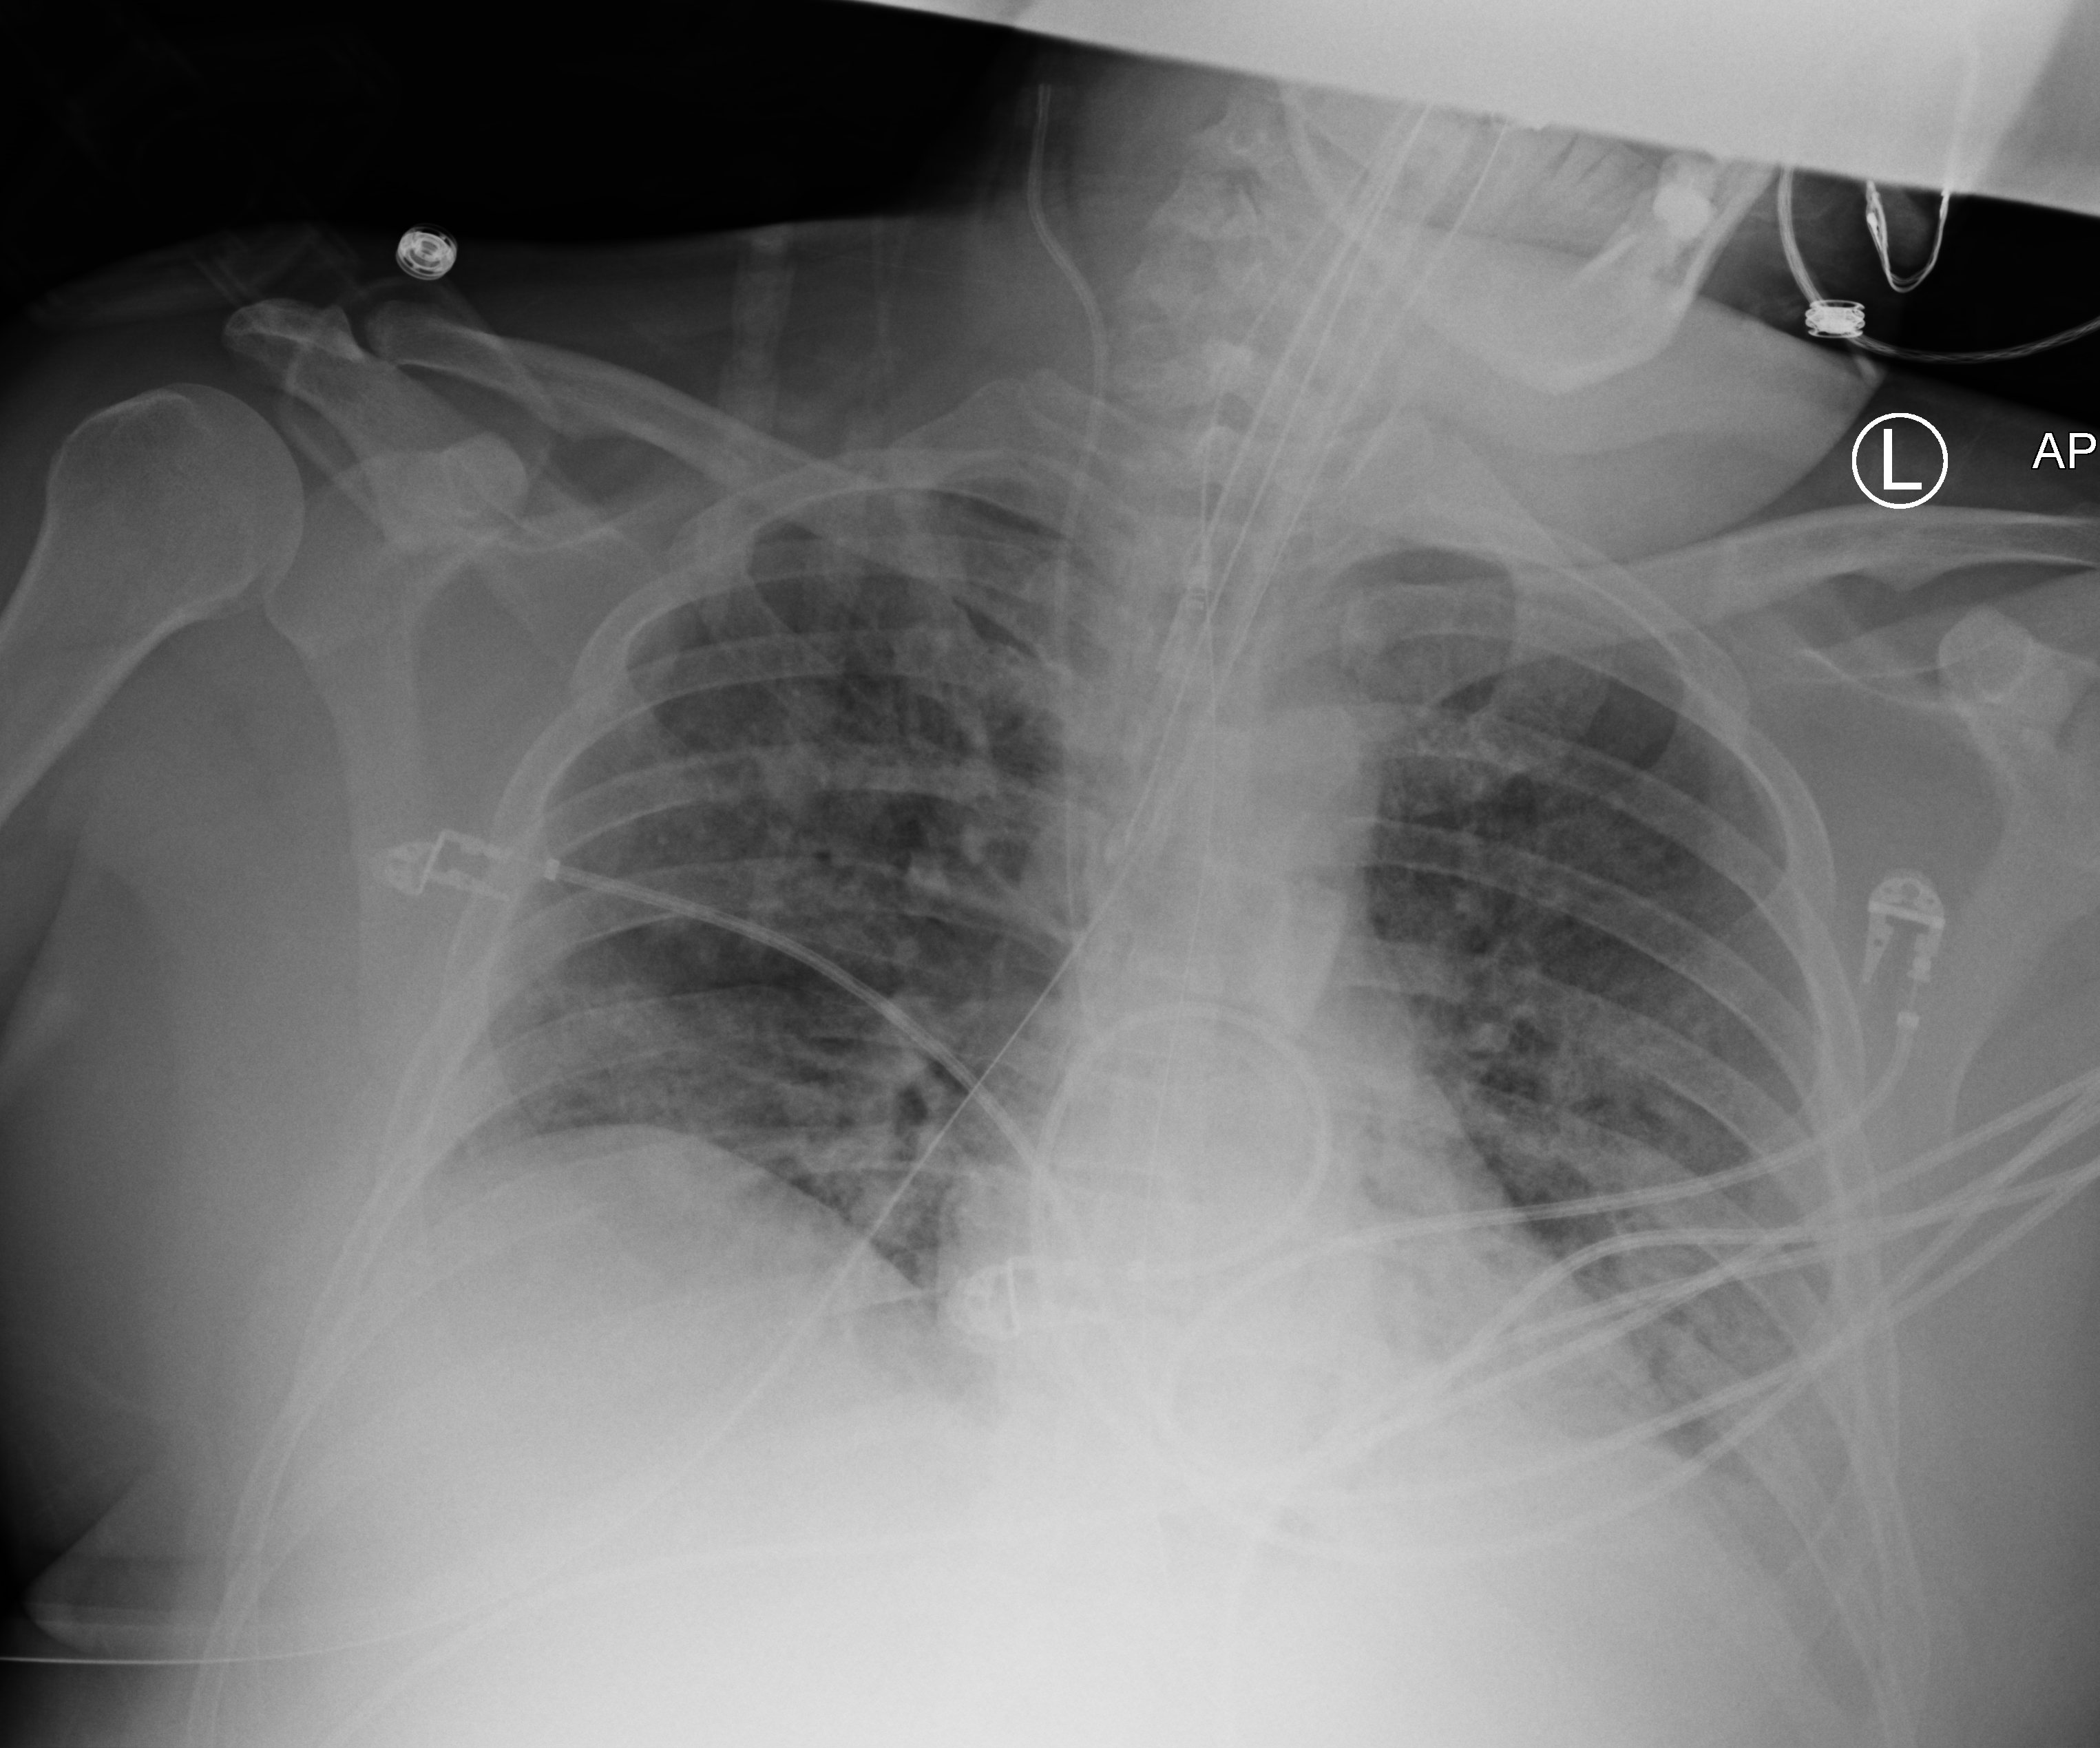
Bedside chest radiograph (computed radiography), anteroposterior (AP) projection. Patient hospitalised with COVID-19; male, aged 18–59 years.
From the hospital-stay record, not from the radiograph (when in the stay this image was taken is not recorded): admitted to intensive care during this hospital stay: yes.